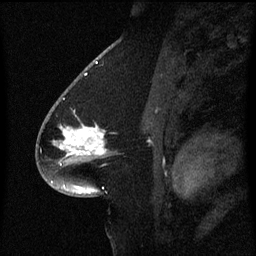
Breast MRI (dynamic contrast-enhanced), one sagittal slice; slice 34 of 60 in the series (ordered by position); dynamic contrast-enhanced series, image 2 of 3 at this slice position (ordered by acquisition); 1.5 T; TE 4.2 ms, TR 8.4 ms; 2 mm slice thickness; 256 × 256 image matrix, field of view 200 × 200 mm. Patient: female, 54 years. From the clinical record (not read from this slice): setting: breast cancer imaged before/during neoadjuvant chemotherapy; receptor status: HR-positive, HER2-negative.
Outlined on this slice (semi-automatic segmentation, software-assisted and operator-edited):
- analysis volume of interest (the breast-tissue region the enhancement analysis was run in; not a lesion): bounding box (x1, y1, x2, y2) in pixels: (46, 100, 111, 167)
- tumour enhancement mask (voxels above the 70 % enhancement threshold inside the analysis volume of interest): (62, 126, 106, 155)